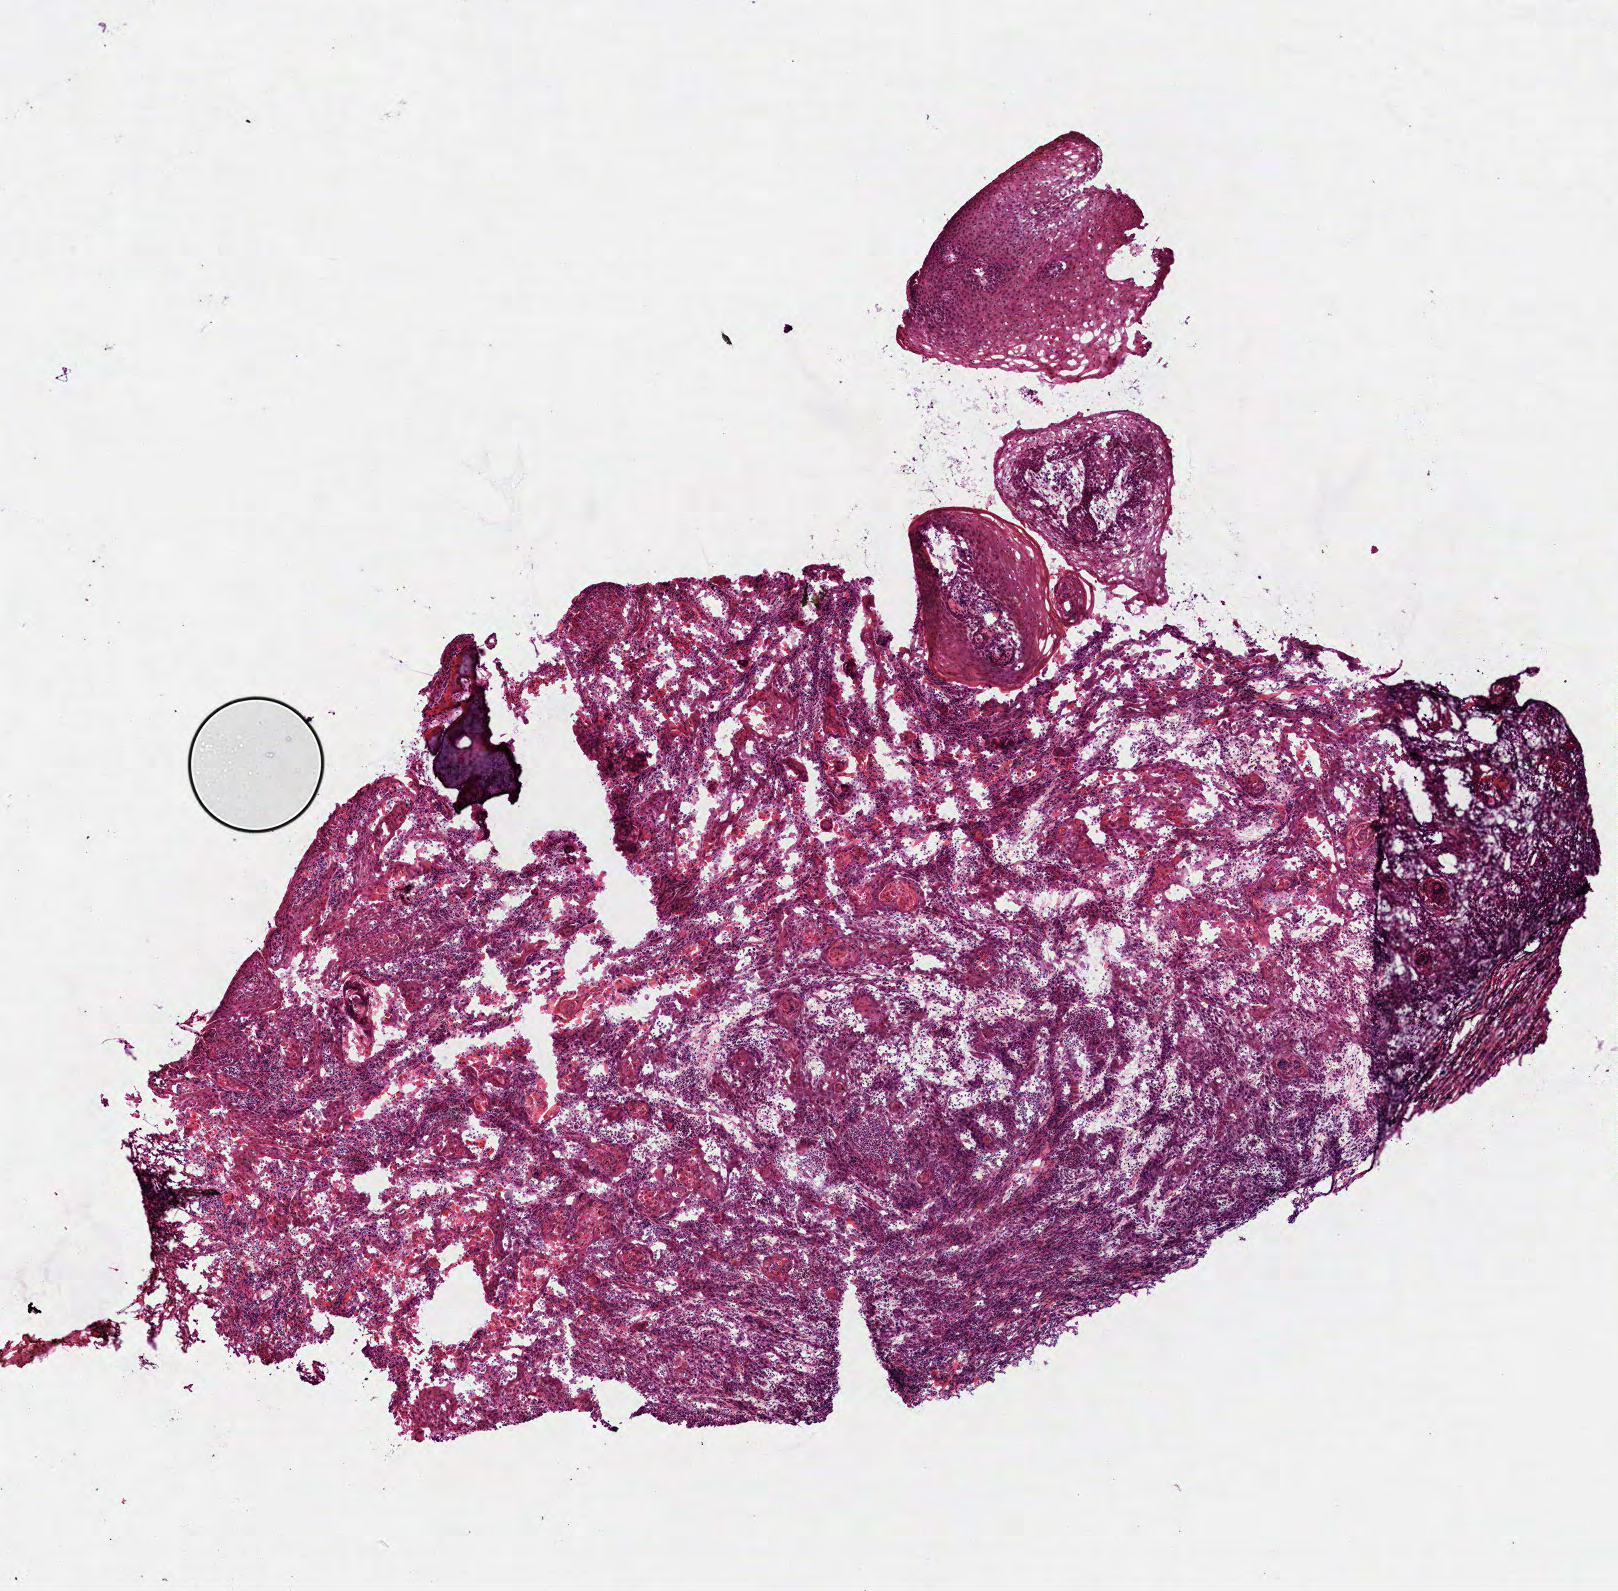
Digitized Hematoxylin and eosin (H&E) stained tissue section (whole slide), low-resolution overview of the scanned area, about 6.5 x 6.4 mm (slide scanned at 40x); frozen section; head and neck, primary tumour sample. Female patient; age at initial diagnosis 74 years. Composition of this section per pathologist review: tumour cells 85%, tumour nuclei 60%.
Pathologic diagnosis: Squamous cell carcinoma, NOS (overlapping lesion of lip, oral cavity and pharynx).